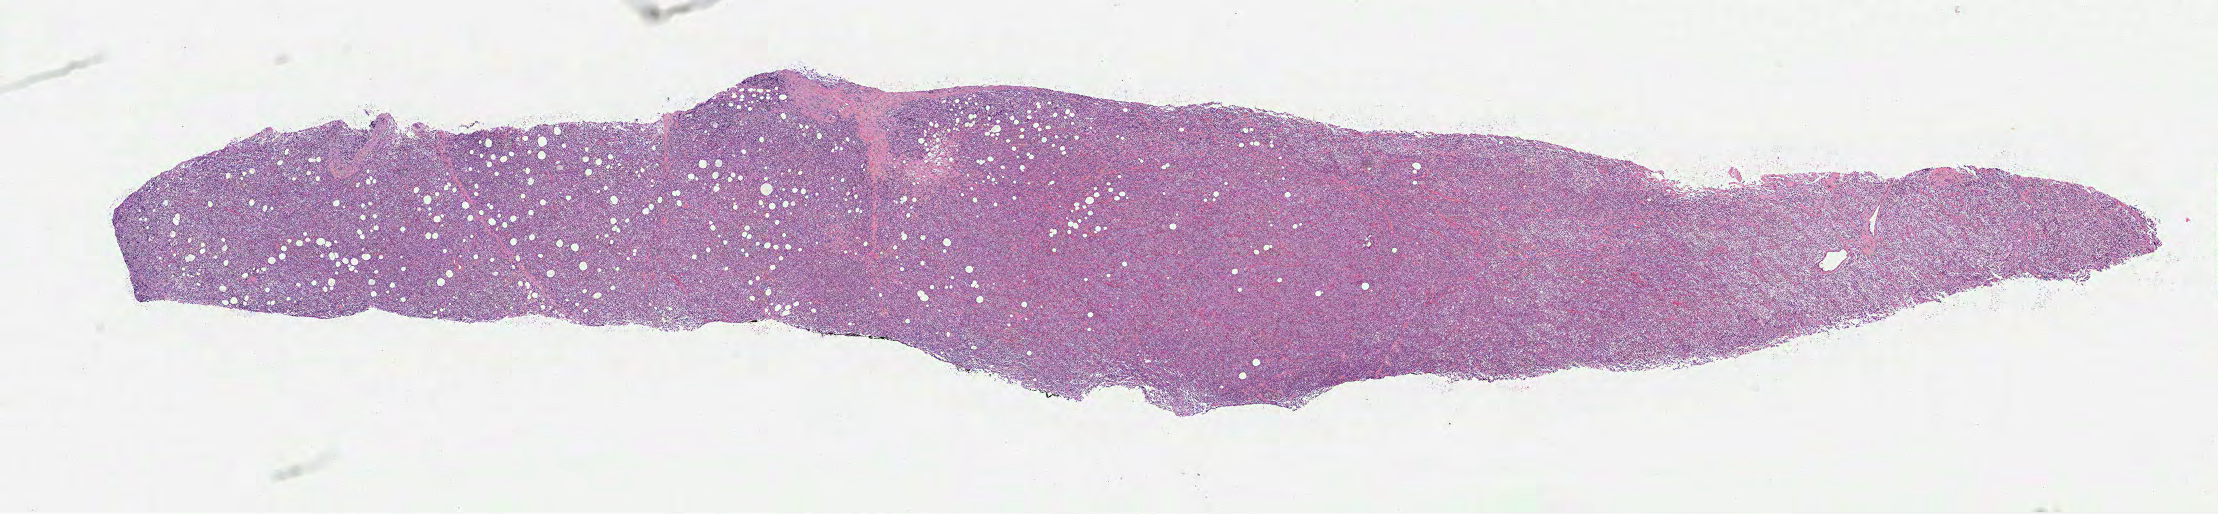
Whole-slide histology image, Hematoxylin and eosin (H&E) stained — whole scanned area (about 17.9 x 4.1 mm) shown as a low-resolution overview; formalin-fixed paraffin-embedded (FFPE) diagnostic section; sample: primary tumour, lymphoid tissue. Female, age 70 years at initial diagnosis.
Pathologic diagnosis: Diffuse large B-cell lymphoma, NOS.